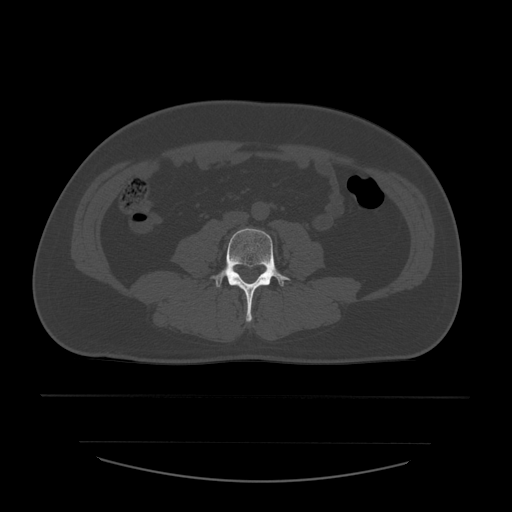
CT including the spine, one axial slice. Position 148 of 532 along the scan axis. 120 kVp. Bone window (W 1800 / L 400 HU). 1.25 mm slice thickness. 512 × 512 image matrix, field of view 441 × 441 mm. Patient age 44 years. Case-level facts recorded for this patient, not image findings: primary cancer: soft tissue sarcoma.
Outlined on this slice (semi-automatic segmentation, software-assisted and operator-edited):
- L4 vertebra: bounding box (x1, y1, x2, y2) in pixels: (211, 229, 291, 322)